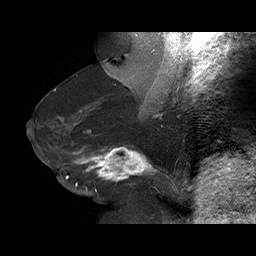
Breast MRI (dynamic contrast-enhanced), one sagittal slice; position 37 of 75 along the scan axis; dynamic contrast-enhanced series, time point 2 of 6 at this slice position (early post-contrast); 1.5 T; TE 4.5 ms, TR 32.4 ms; 3 mm slice thickness; 256 × 256 image matrix, field of view 180 × 180 mm. Female patient. From the clinical record (not read from this slice): setting: breast cancer imaged before/during neoadjuvant chemotherapy; receptor status: HR-positive, HER2-negative.
Annotated regions visible in this slice (semi-automatically segmented with operator editing):
- analysis volume of interest (the breast-tissue region the enhancement analysis was run in; not a lesion): box from (x=58, y=134) to (x=166, y=191) px
- tumour enhancement mask (voxels above the 100 % enhancement threshold inside the analysis volume of interest): (x=65, y=146)–(x=157, y=181)